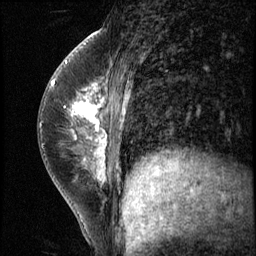
Breast MRI (dynamic contrast-enhanced), one sagittal slice. Position 24 of 56 along the scan axis. 3 images stored at this slice position (order not interpretable as contrast timing). 1.5 T. TE 4.2 ms, TR 8.7 ms. 2.5 mm slice thickness. 256 × 256 image matrix, field of view 180 × 180 mm. Female patient, age 35 years. Case-level facts recorded for this patient, not image findings: setting: breast cancer imaged before/during neoadjuvant chemotherapy; receptor status: HER2-positive.
Outlined on this slice (semi-automatically segmented with operator editing):
- analysis volume of interest (the breast-tissue region the enhancement analysis was run in; not a lesion): bounding box [x1, y1, x2, y2] px = [58, 84, 134, 186]
- tumour enhancement mask (voxels above the 140 % enhancement threshold inside the analysis volume of interest): [63, 84, 126, 179]